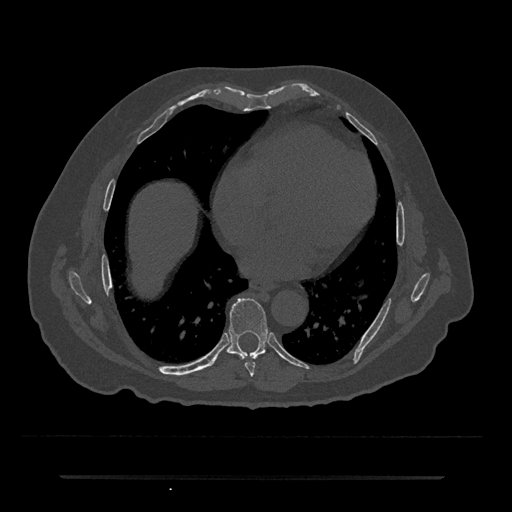
CT including the spine, one axial slice; slice 352 of 797 in the series (ordered by position); reconstruction kernel Br40s/3; 120 kVp; bone window (W 1800 / L 400 HU); 512 × 512 image matrix, field of view 437 × 437 mm. Male patient, age 69 years. From the clinical record (not read from this slice): primary cancer: prostate.
Structures marked on this image (semi-automatically segmented with operator editing):
- T7 vertebra: box from (x=245, y=362) to (x=255, y=376) px
- T8 vertebra: (x=226, y=298)–(x=268, y=359)